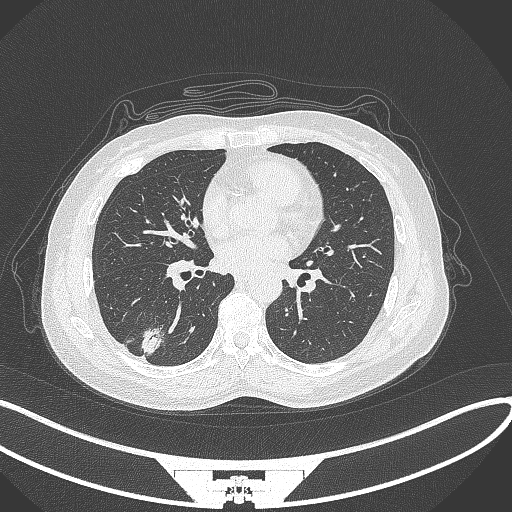
Chest CT, one axial slice; slice 136 of 352 in the series (ordered by position); reconstruction kernel B70f; lung window (W 1500 / L -600 HU); 512 × 512 image matrix, field of view 400 × 400 mm. Patient: female, 55 years. From the clinical record (not read from this slice): clinical TNM (as recorded): T1c N1 M0.
Annotated regions visible in this slice (bounding box drawn by a radiologist):
- lung tumour (recorded histology: adenocarcinoma): bounding box <140,321,167,358> (left, top, right, bottom; pixels)